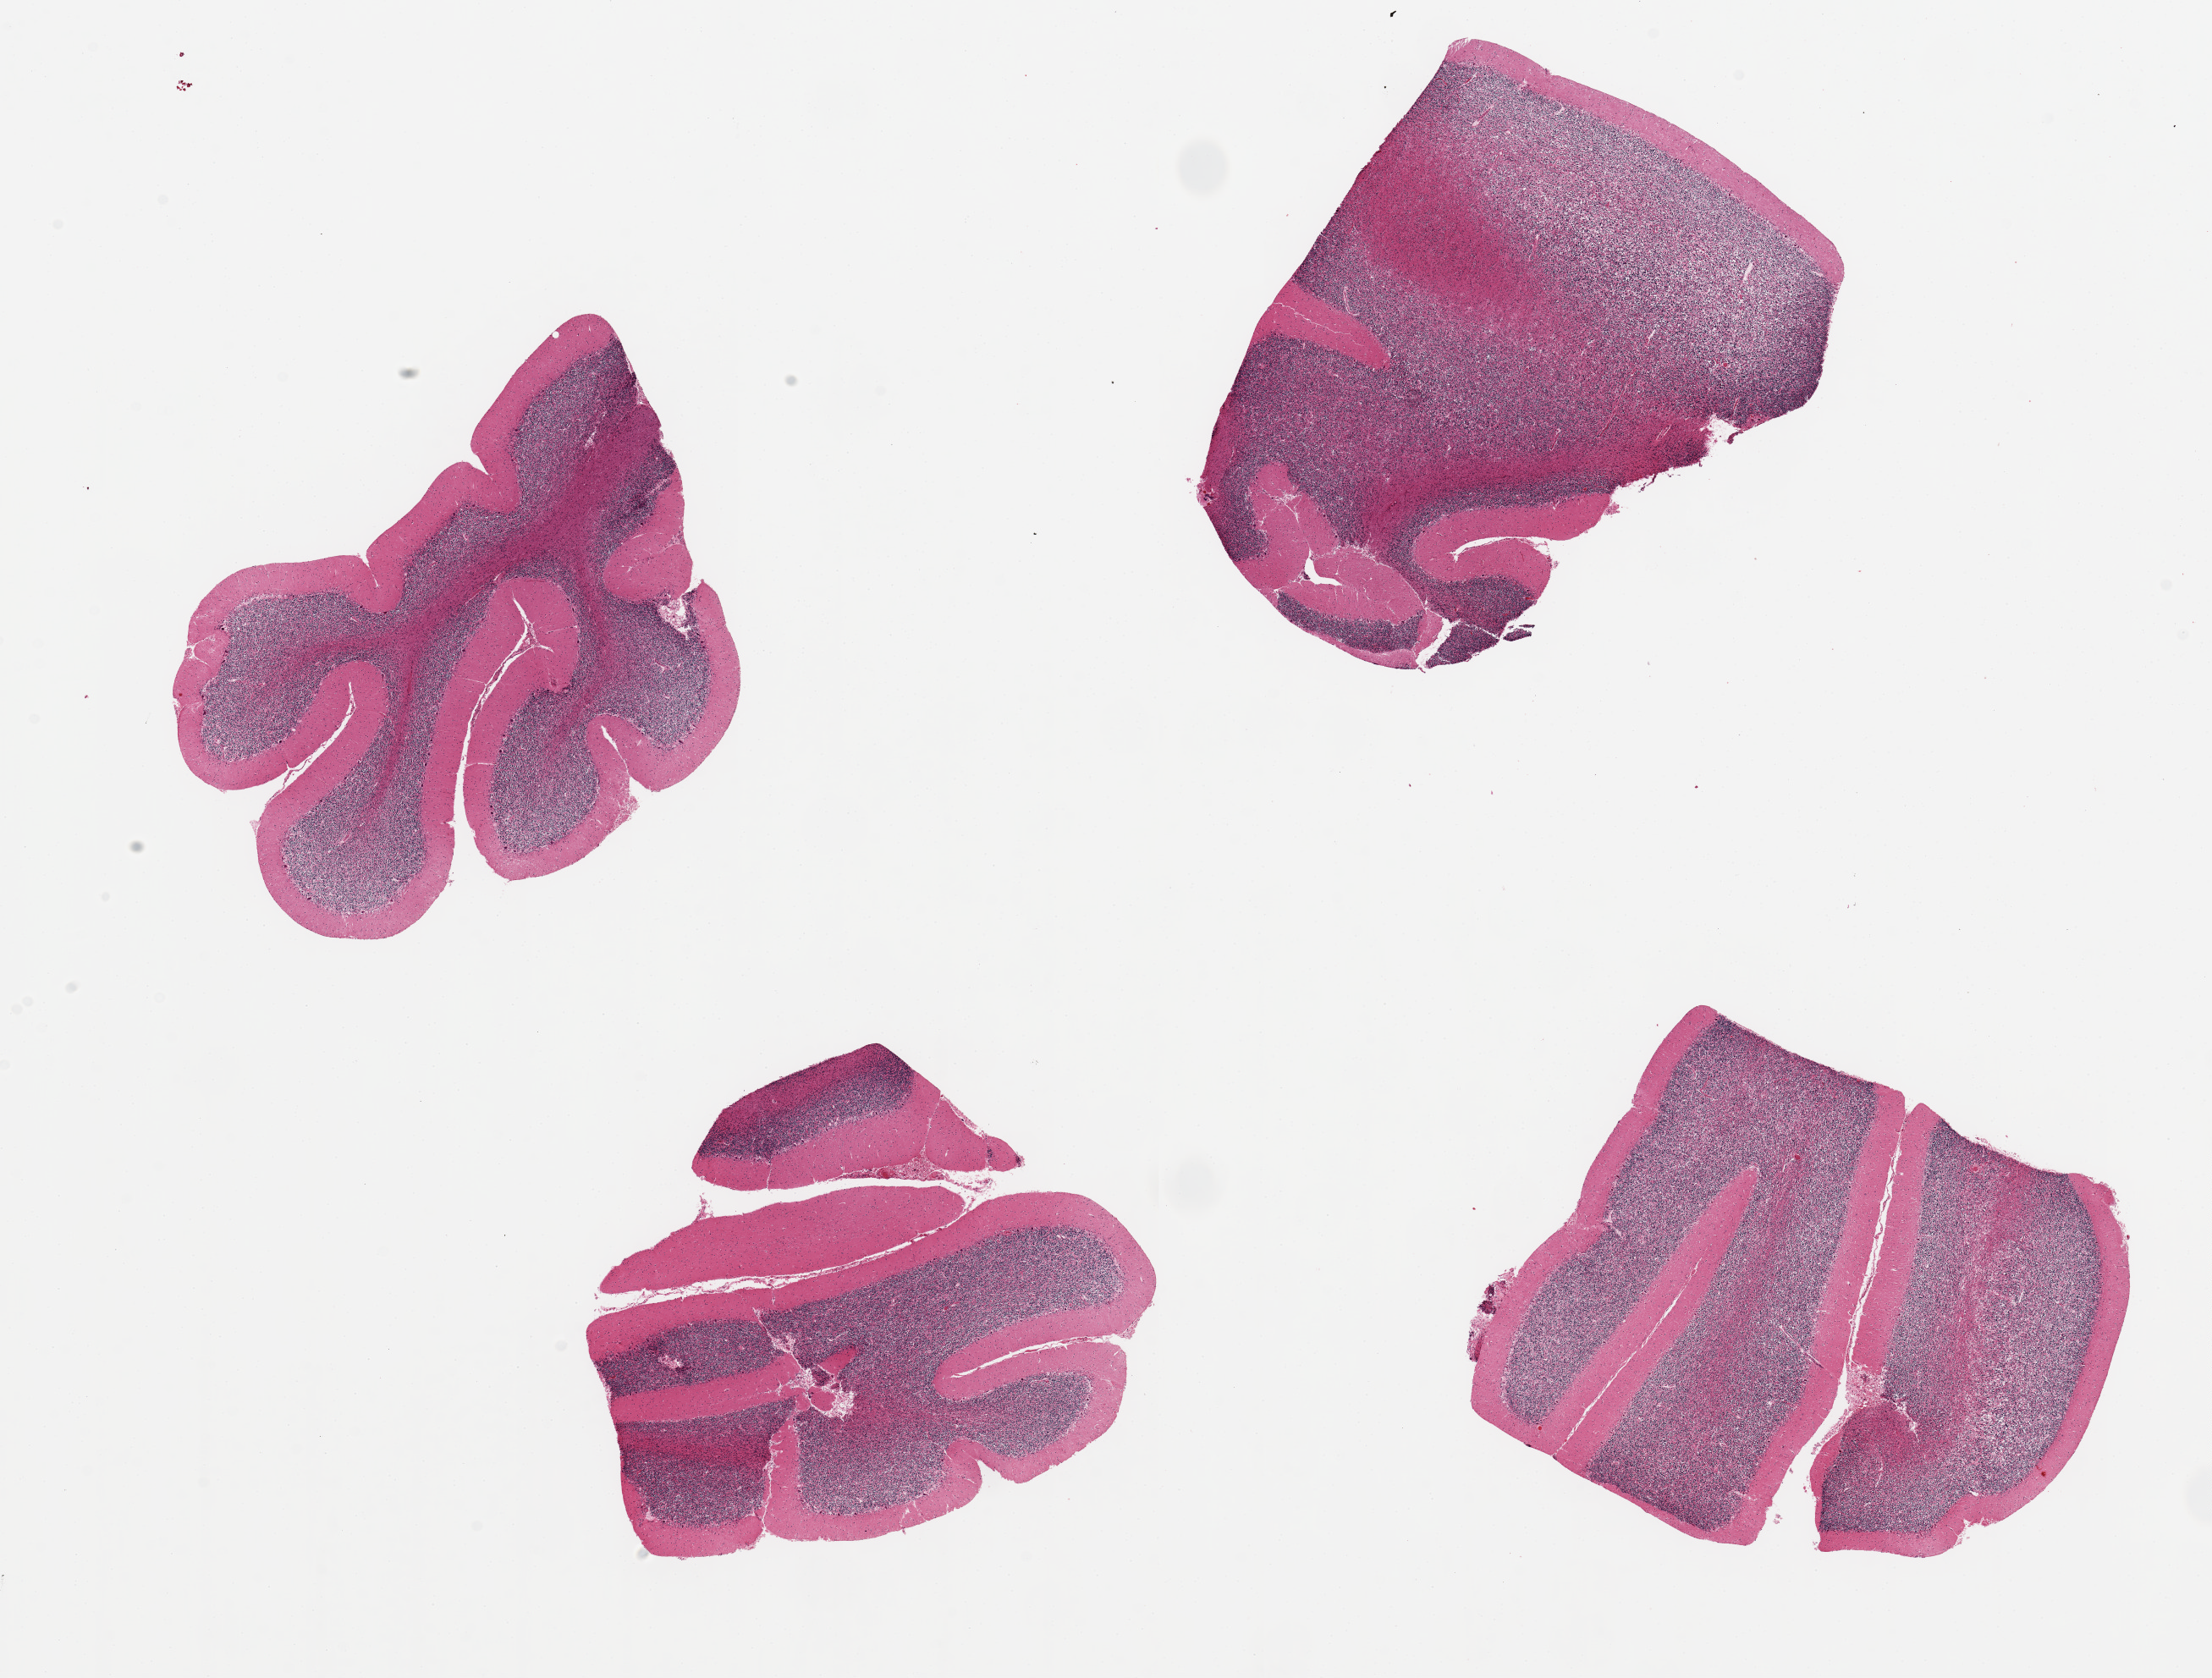
Digitized hematoxylin and eosin (H&E)-stained section, brightfield — shown as a low-resolution overview of the whole scanned area (about 20.7 x 15.7 mm, slide scanned at 20x), PAXgene-fixed, paraffin-embedded tissue, target tissue: cerebellum, tissue donor sample. Donor: male.
Pathologist's review note for this sample: 4 aliquots, ~ 5x4mm. Granular layer most autolyzed.